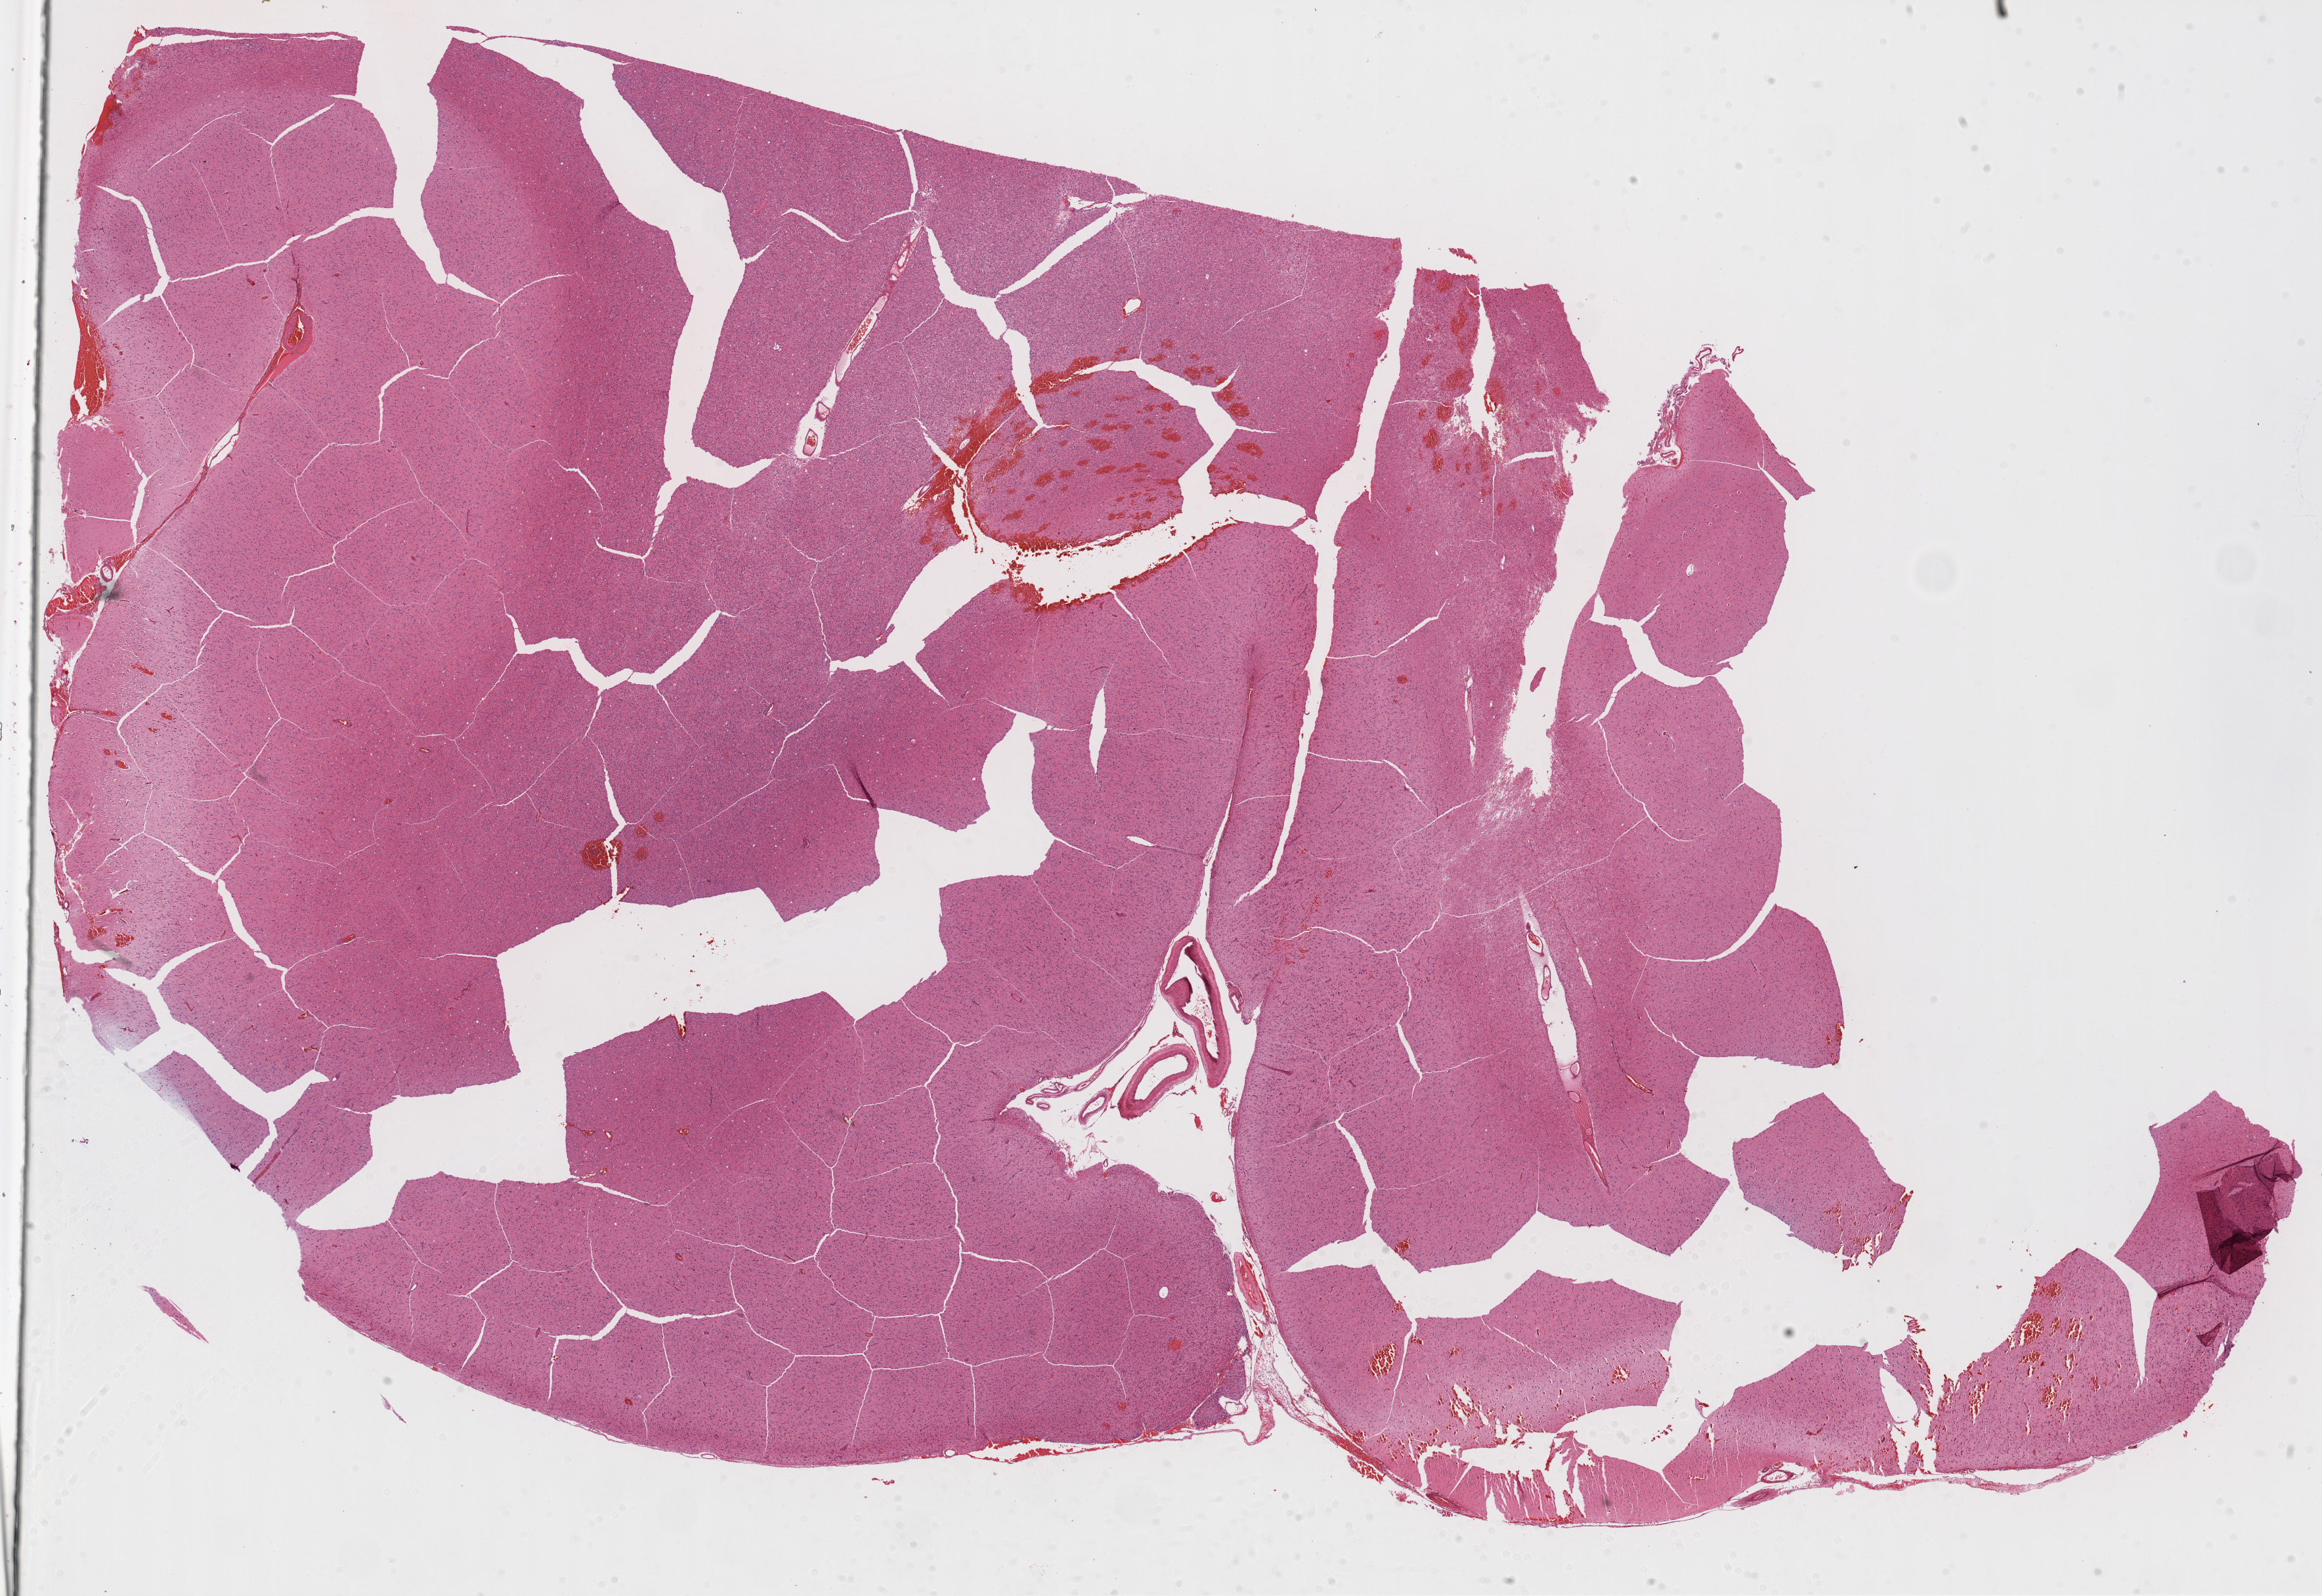
H&E-stained whole-slide image, low-resolution overview of the scanned area, about 28.5 x 19.6 mm, FFPE section, primary tumour sample from the brain. Male patient; age at initial diagnosis 66 years.
Diagnosis: Glioblastoma.